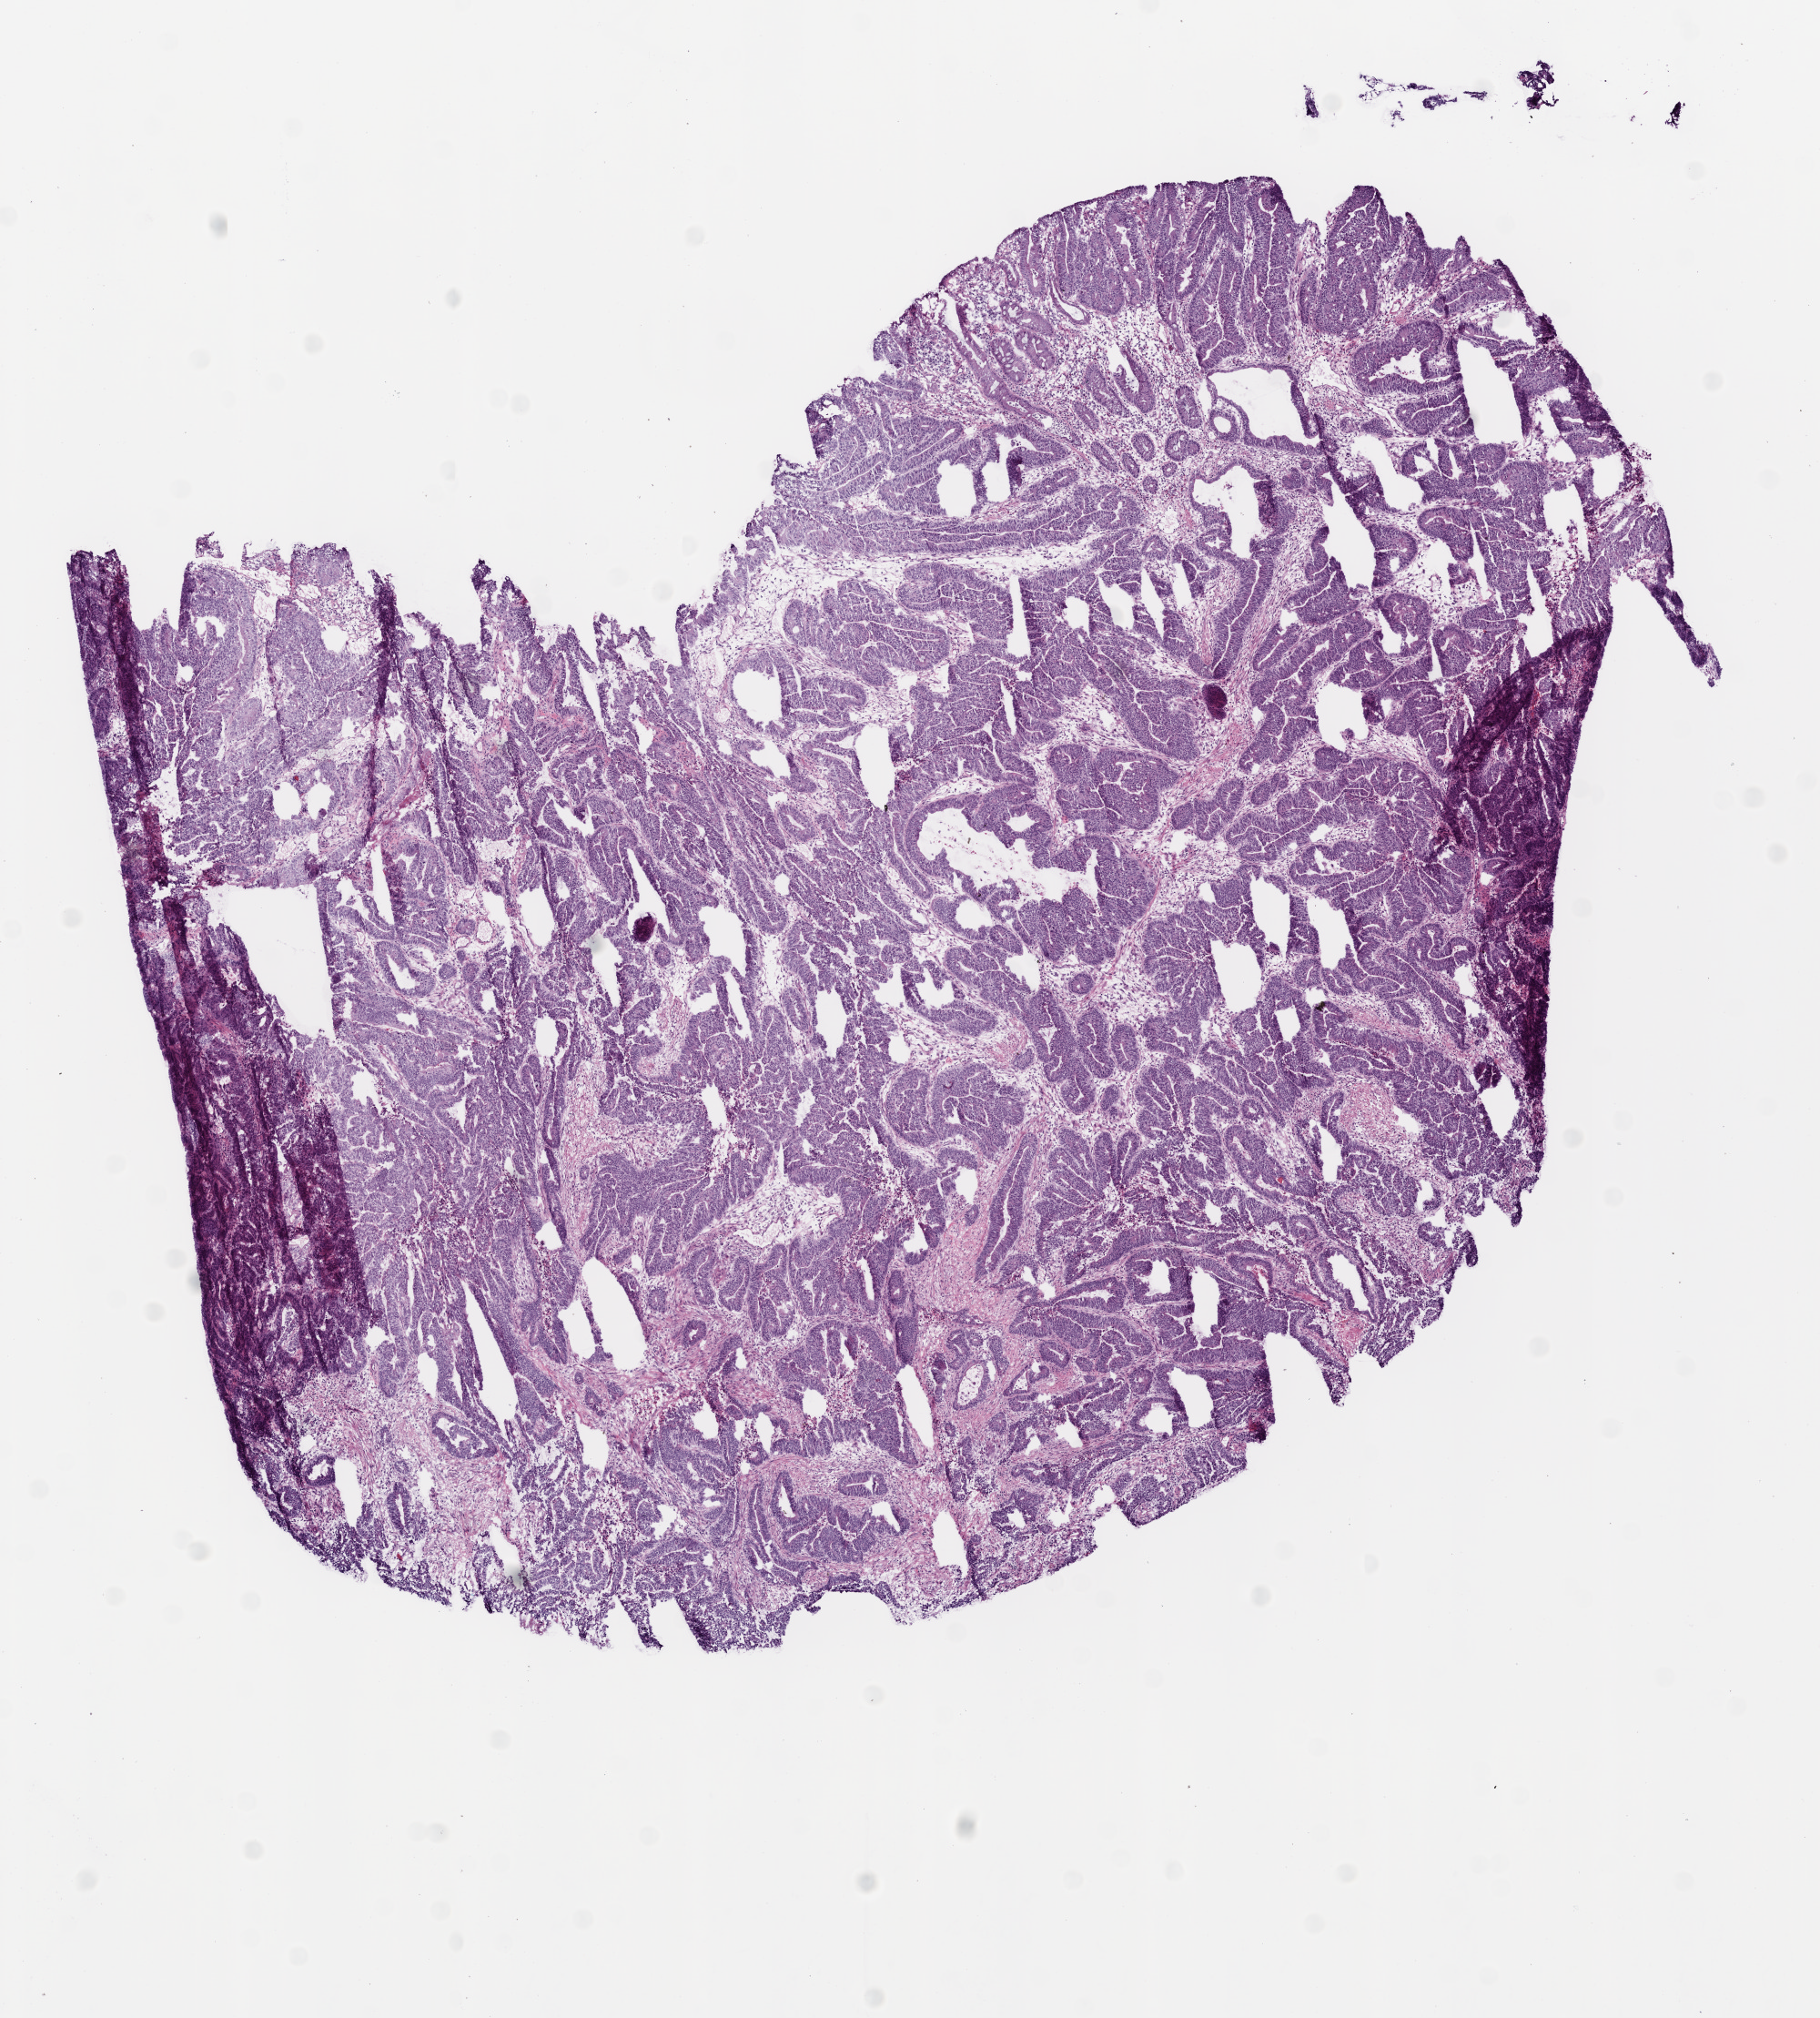
Whole-slide histology image, H&E — whole scanned area (about 8.0 x 8.9 mm, slide scanned at 20x) shown as a low-resolution overview. Frozen section. Primary tumour sample from the rectum. Female patient; age at initial diagnosis 78 years. Composition of this section per pathologist review: tumour cells 85%, tumour nuclei 75%, normal cells 0%, stromal cells 10%, necrosis 5%.
- AJCC pathologic stage: III (5th edition)
- lymph nodes positive (case pathology): 2 of 25 examined
- pathologic diagnosis: Adenocarcinoma, NOS (rectosigmoid junction)